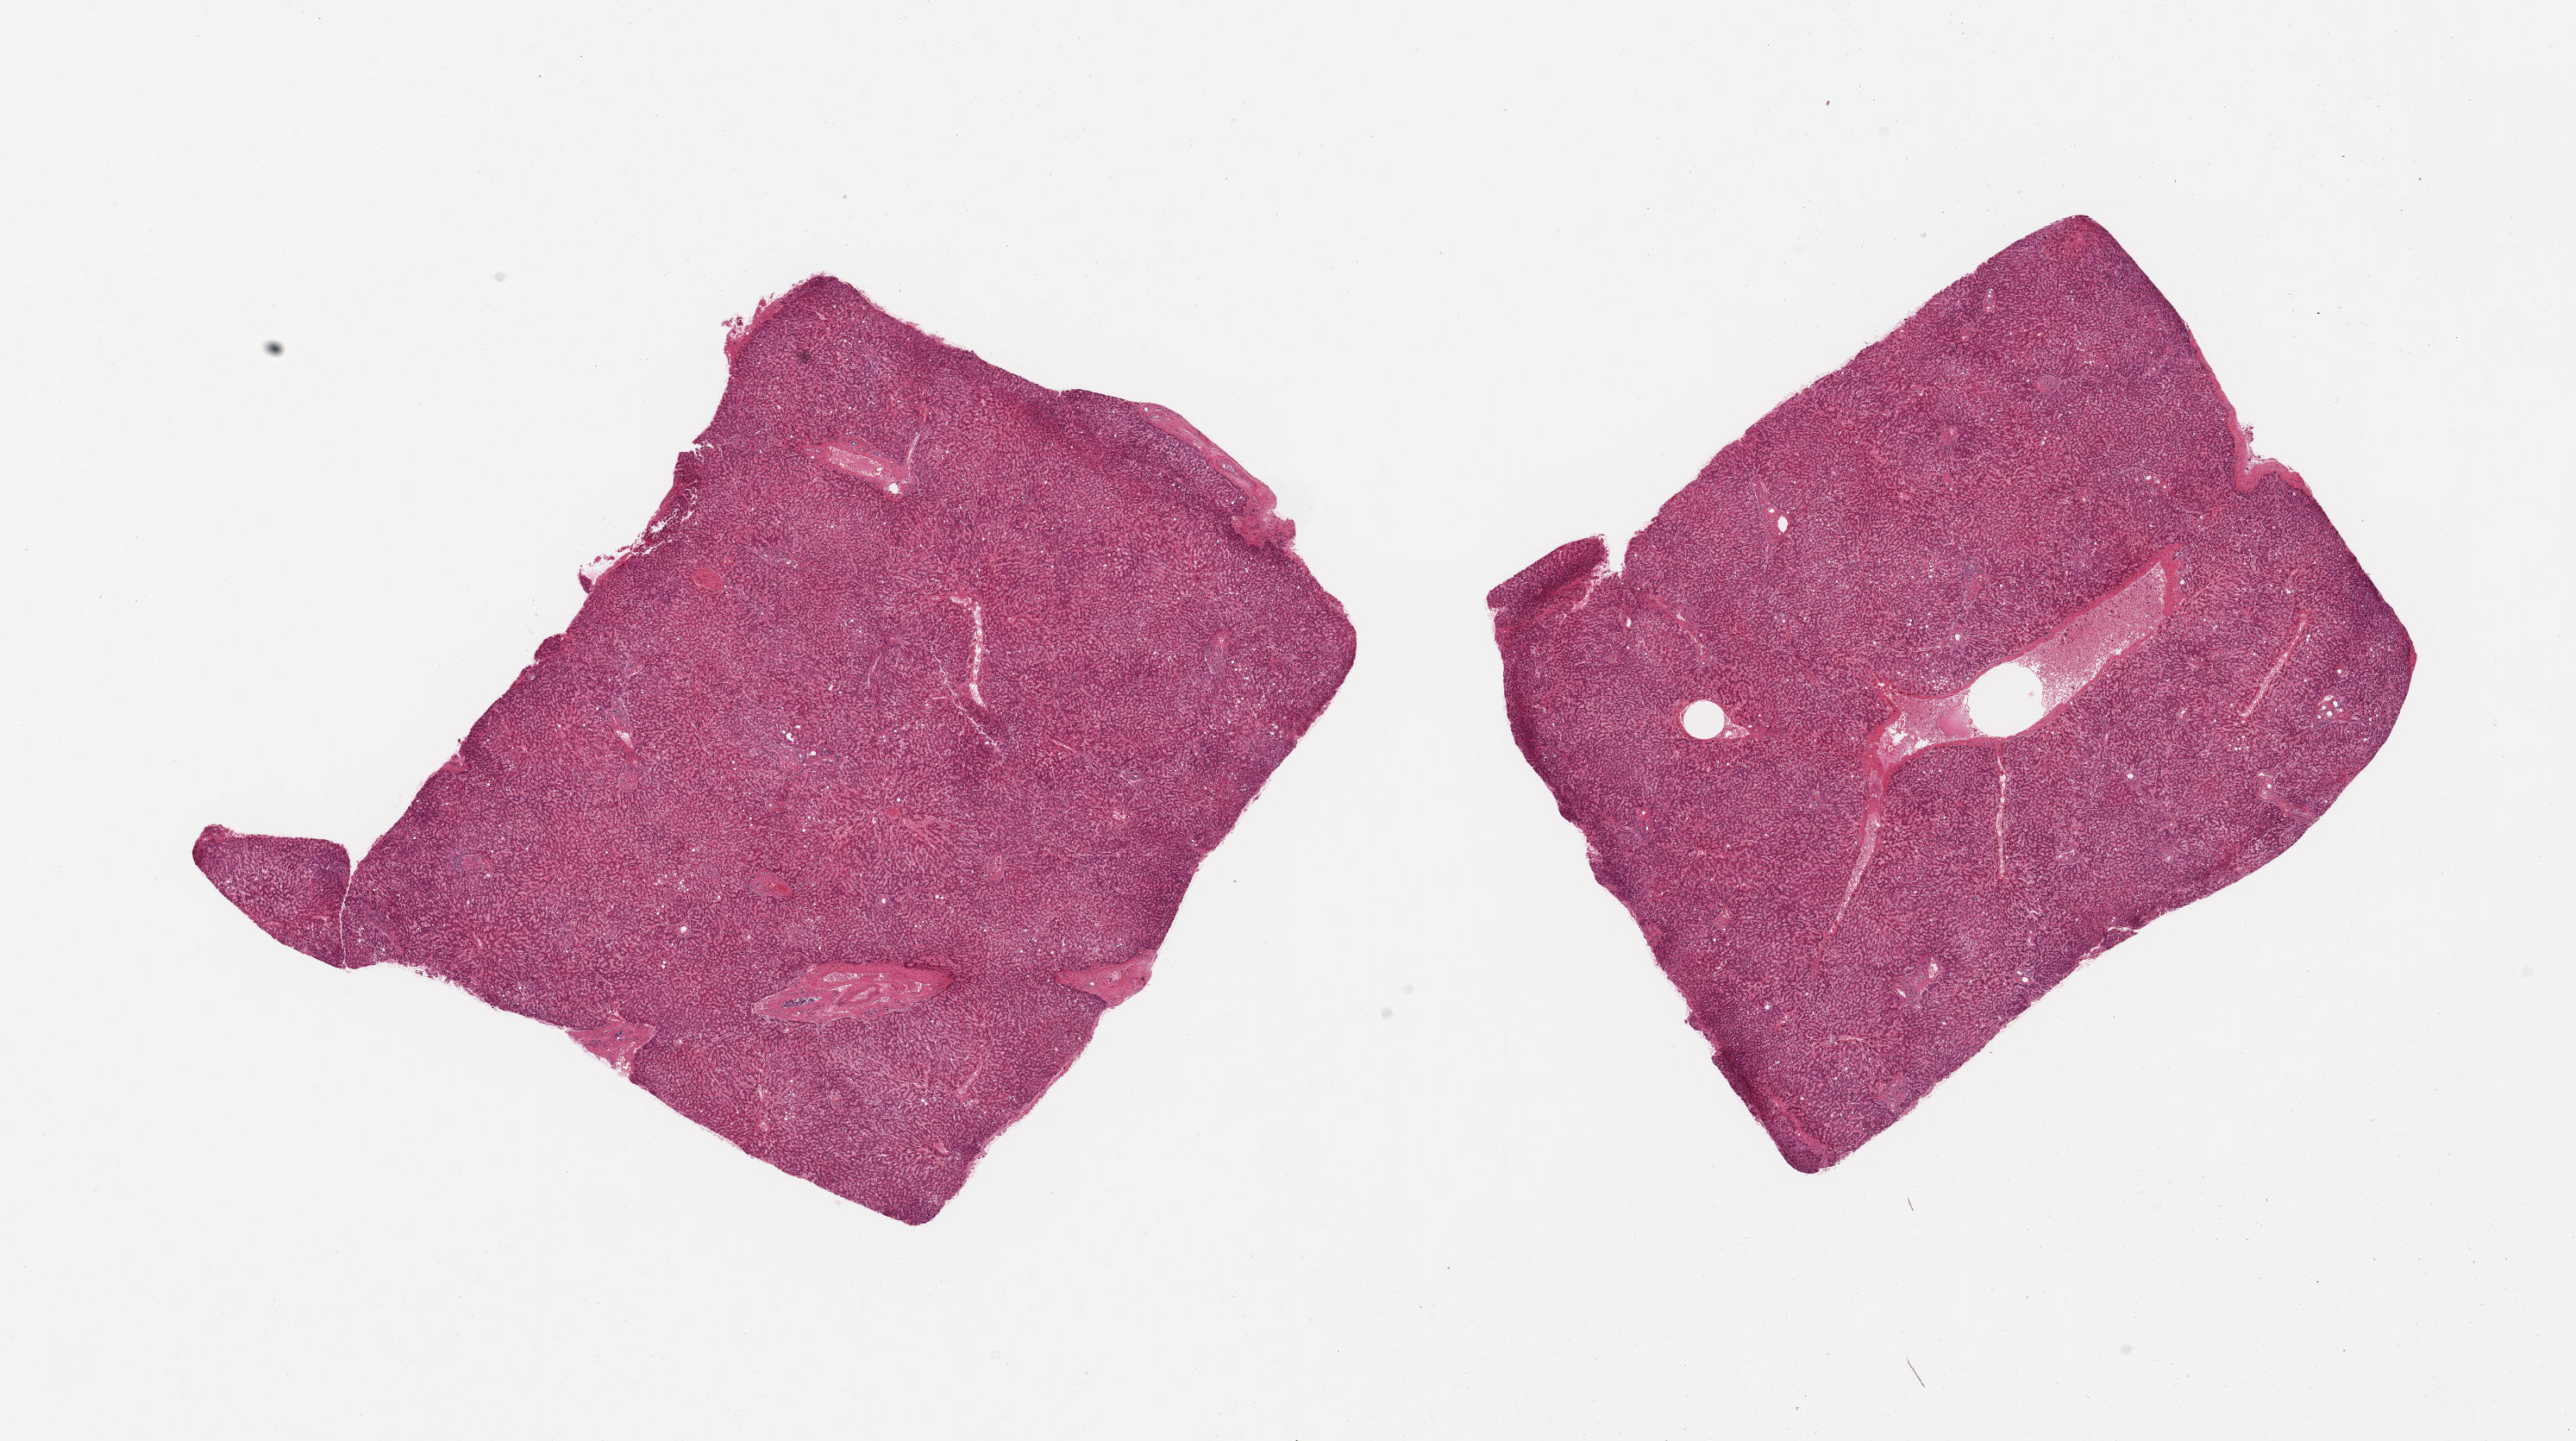
Whole-slide image, H&E stain, a low-resolution overview of the entire scanned area, about 23.6 x 13.2 mm. PAXgene-fixed, paraffin-embedded tissue. Sampled site (target tissue): liver. Donor tissue sample. Donor: female.
* pathologist's review note for this sample: 2 pieces, moderate passive congestion